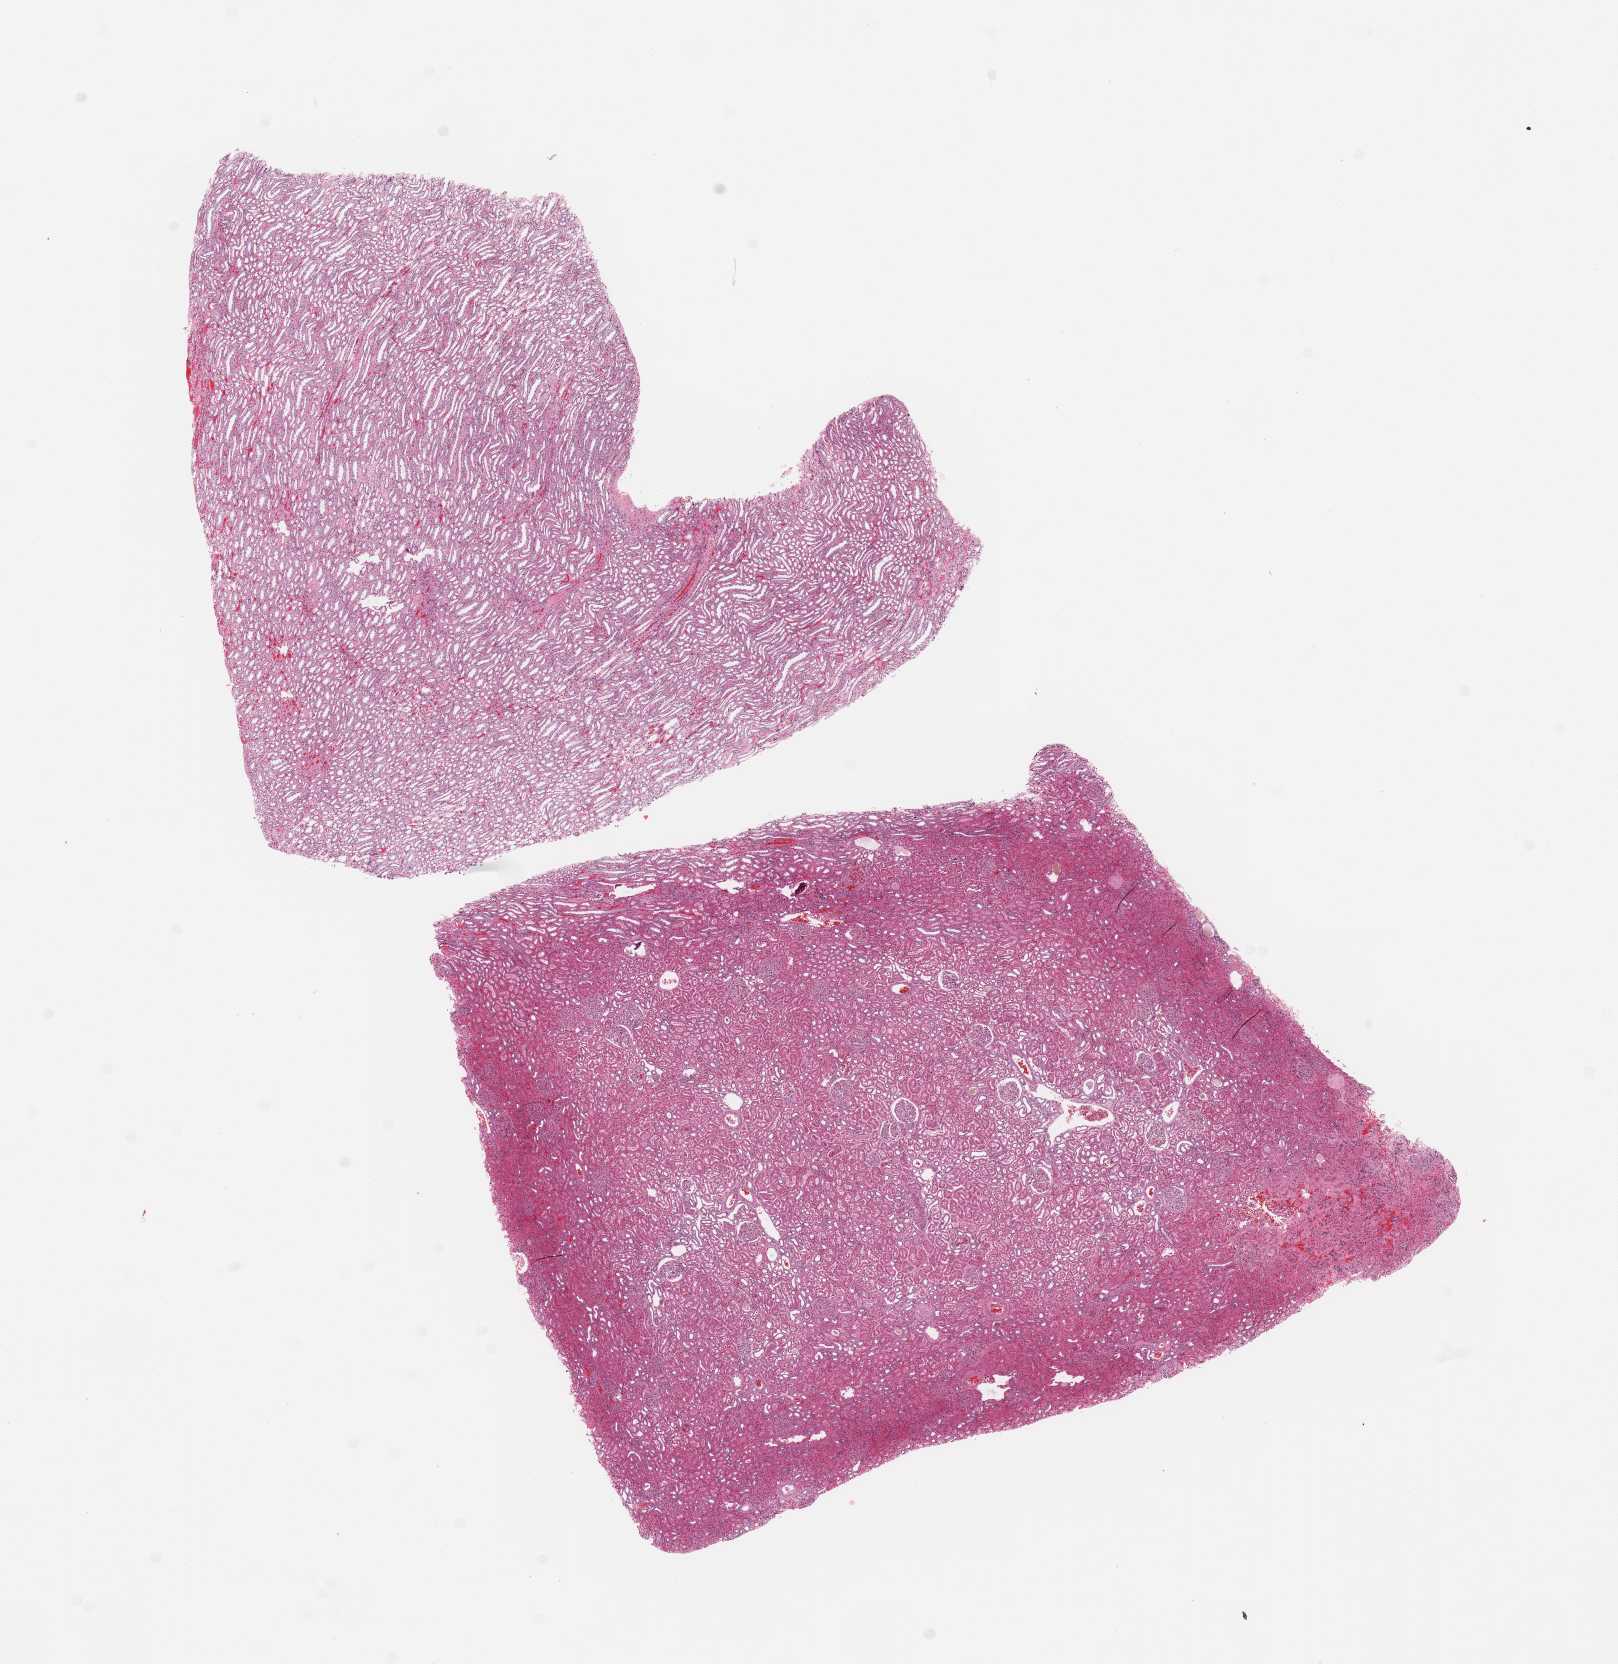
Digitized Hematoxylin and eosin (H&E) stained tissue section (whole slide) — shown as a low-resolution overview of the whole scanned area (about 12.8 x 13.2 mm, acquisition: 20x scan), normal (non-tumour) tissue sample, sampled site: kidney. Male, 30 y/o.
• this section: normal (non-tumour) tissue from the same patient
• patient diagnosis: Renal cell carcinoma, NOS